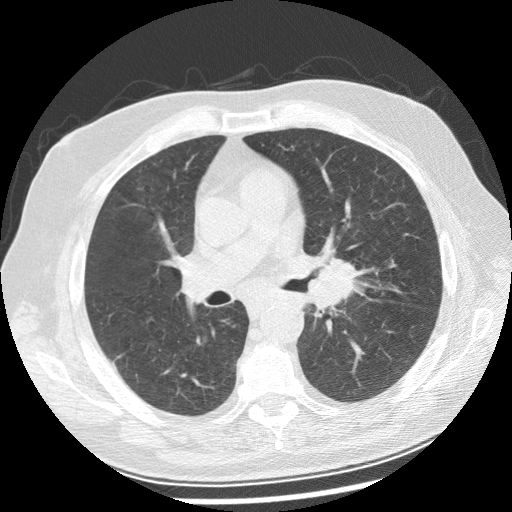
Low-dose screening chest CT, axial slice. First (baseline) screen. Lung window (W 1500 / L -600 HU). Slice 108 of 250 in the series. Male, age 70 years at enrolment.
Lesion marked by an expert reader, bounding box <284,241,366,312> (left, top, right, bottom; pixels). Screening reader's record for this exam: no non-calcified nodule ≥4 mm recorded. Official screen result: positive, change unspecified: nodule(s) >= 4 mm or enlarging nodule(s), mass(es), or other non-specific abnormalities suspicious for lung cancer. Lung cancer was diagnosed 29 days after this screen: squamous cell carcinoma, keratinizing, NOS, left main stem bronchus, moderately differentiated (G2), stage IIIB (AJCC 6th edition), 40 mm at pathology.